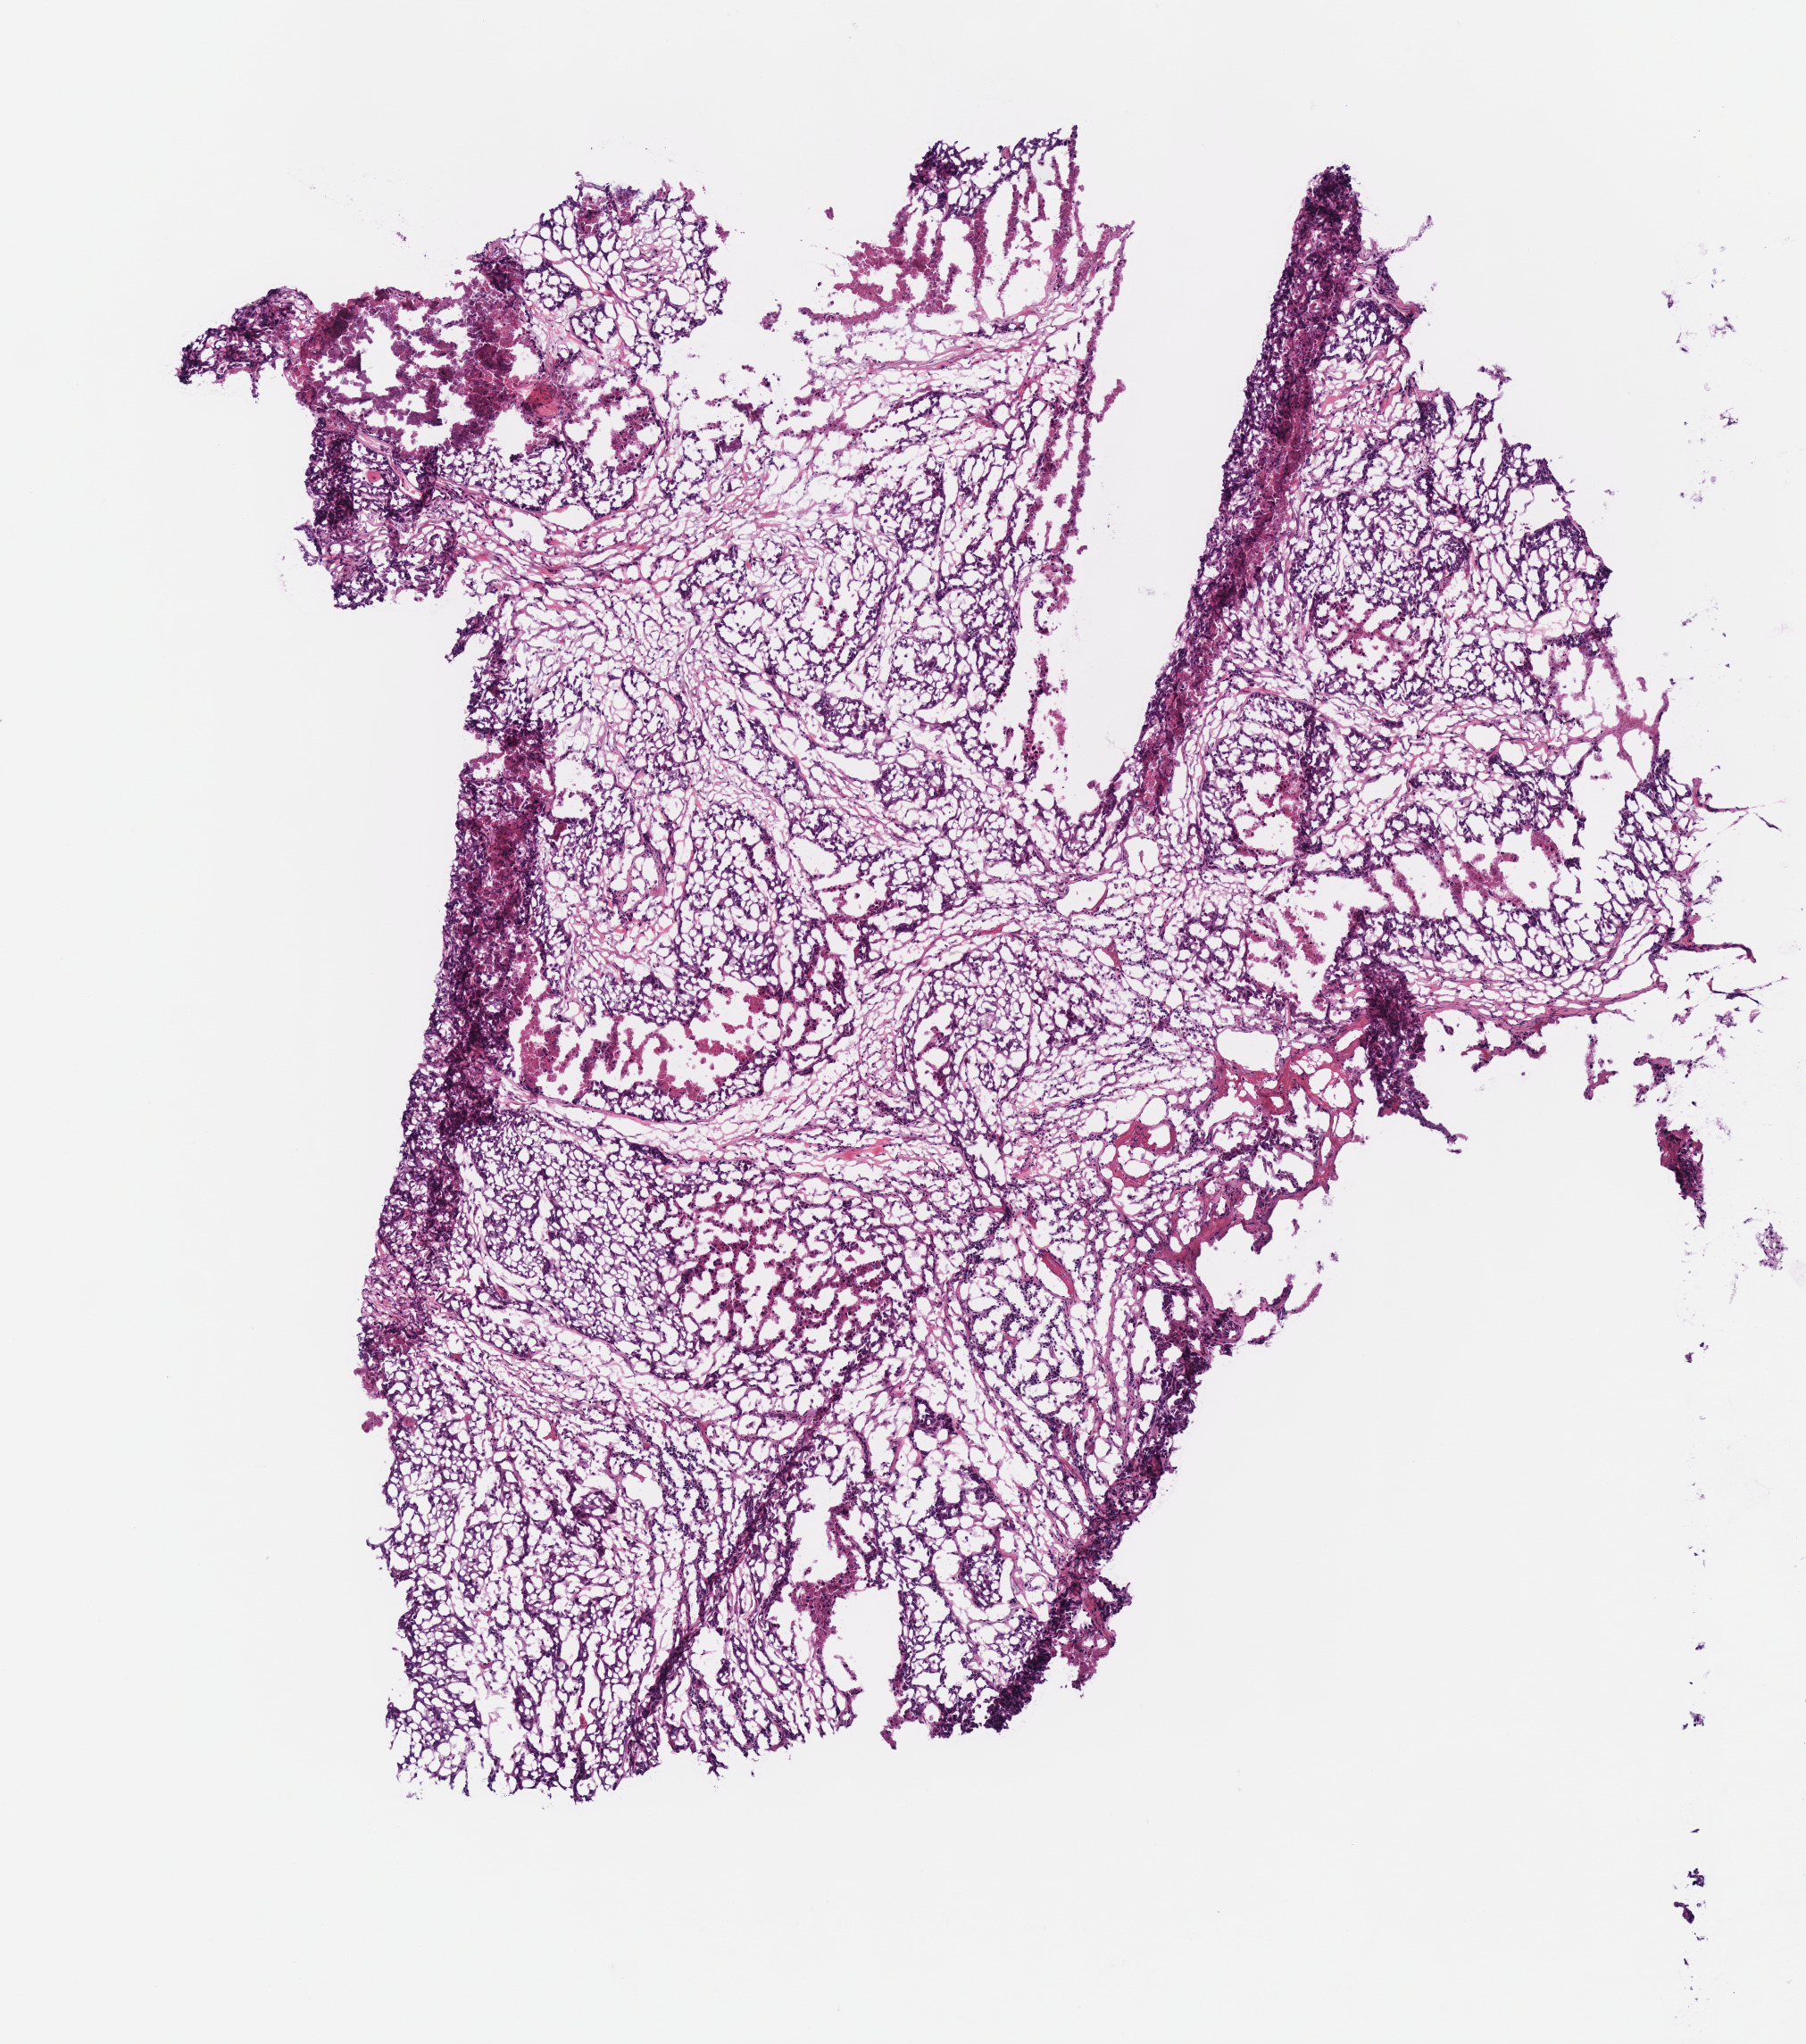
Digitized H&E-stained tissue section (whole slide), low-resolution overview of the scanned area, about 4.0 x 4.5 mm, frozen section, sample: primary tumour, head and neck. Male patient; age at initial diagnosis 67 years. Histologic grade: G2 (moderately differentiated). Pathologist review of this section (percent, as recorded): tumour cells 100%, tumour nuclei 70%, normal cells 0%, stromal cells 0%, necrosis 0%. Inflammatory infiltration, as recorded: lymphocyte infiltration 10%, monocyte infiltration 0%, neutrophil infiltration 0%.
* laterality: right
* TNM: T3 N2b
* AJCC pathologic stage: IVA (7th edition)
* histologic diagnosis: Squamous cell carcinoma, NOS (larynx, NOS)